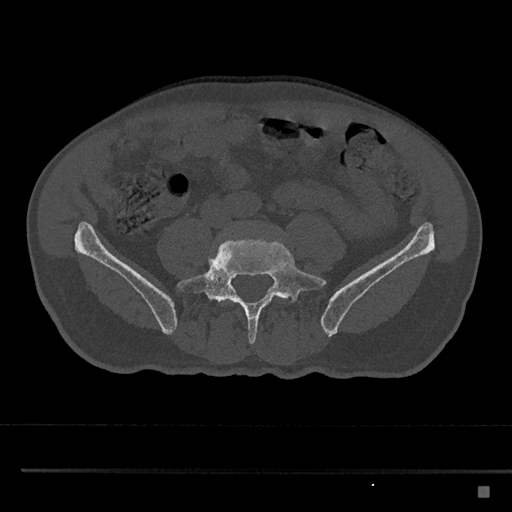
CT including the spine, one axial slice. Position 591 of 797 along the scan axis. Bone window (W 1800 / L 400 HU). 0.5 mm slice thickness. 512 × 512 image matrix, field of view 391 × 391 mm. Male patient, age 59 years. Case-level facts recorded for this patient, not image findings: primary cancer: prostate.
Outlined on this slice (semi-automatic segmentation, software-assisted and operator-edited):
- L5 vertebra: box from (x=177, y=236) to (x=327, y=345) px